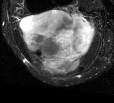
MRI of an extremity soft-tissue mass, one axial slice; position 27 of 44 along the scan axis; T2-weighted fat-saturated; MR volume resampled by the dataset authors to the PET/CT grid (not the native acquisition matrix); 3.27 mm slice thickness; 114 × 103 image matrix, field of view 111 × 101 mm. Female patient. Case-level facts recorded for this patient, not image findings: histological type: liposarcoma; site of the primary tumour: right thigh.
Annotated regions visible in this slice (expert contour drawn on MRI and transferred to this co-registered scan by the dataset authors):
- gross tumour volume (mass): box from (x=18, y=9) to (x=96, y=74) px